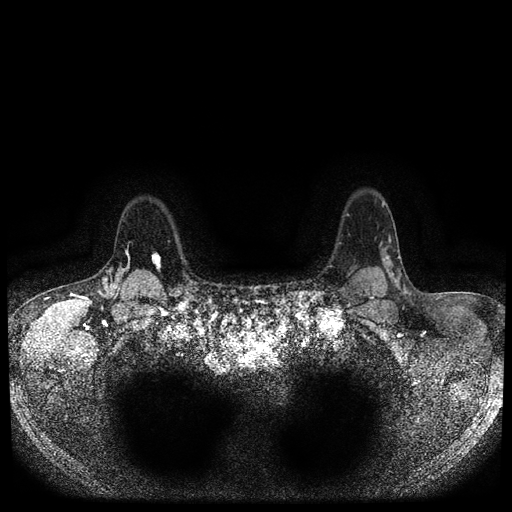
Breast MRI (dynamic contrast-enhanced, multi-phase), one axial slice; position 82 of 116 along the scan axis; dynamic contrast-enhanced series, time point 2 of 5 at this slice position (early post-contrast); 1.5 T; TE 2.6 ms, TR 5.4 ms; 2 mm slice thickness; 512 × 512 image matrix, field of view 340 × 340 mm. Female patient, age 47 years.
Structures marked on this image (semi-automatically segmented with operator editing):
- breast lesion (labelled 'tumour' in the annotation; benign lesions carry a separate 'benign' label): bounding box (x1, y1, x2, y2) in pixels: (148, 250, 163, 273)